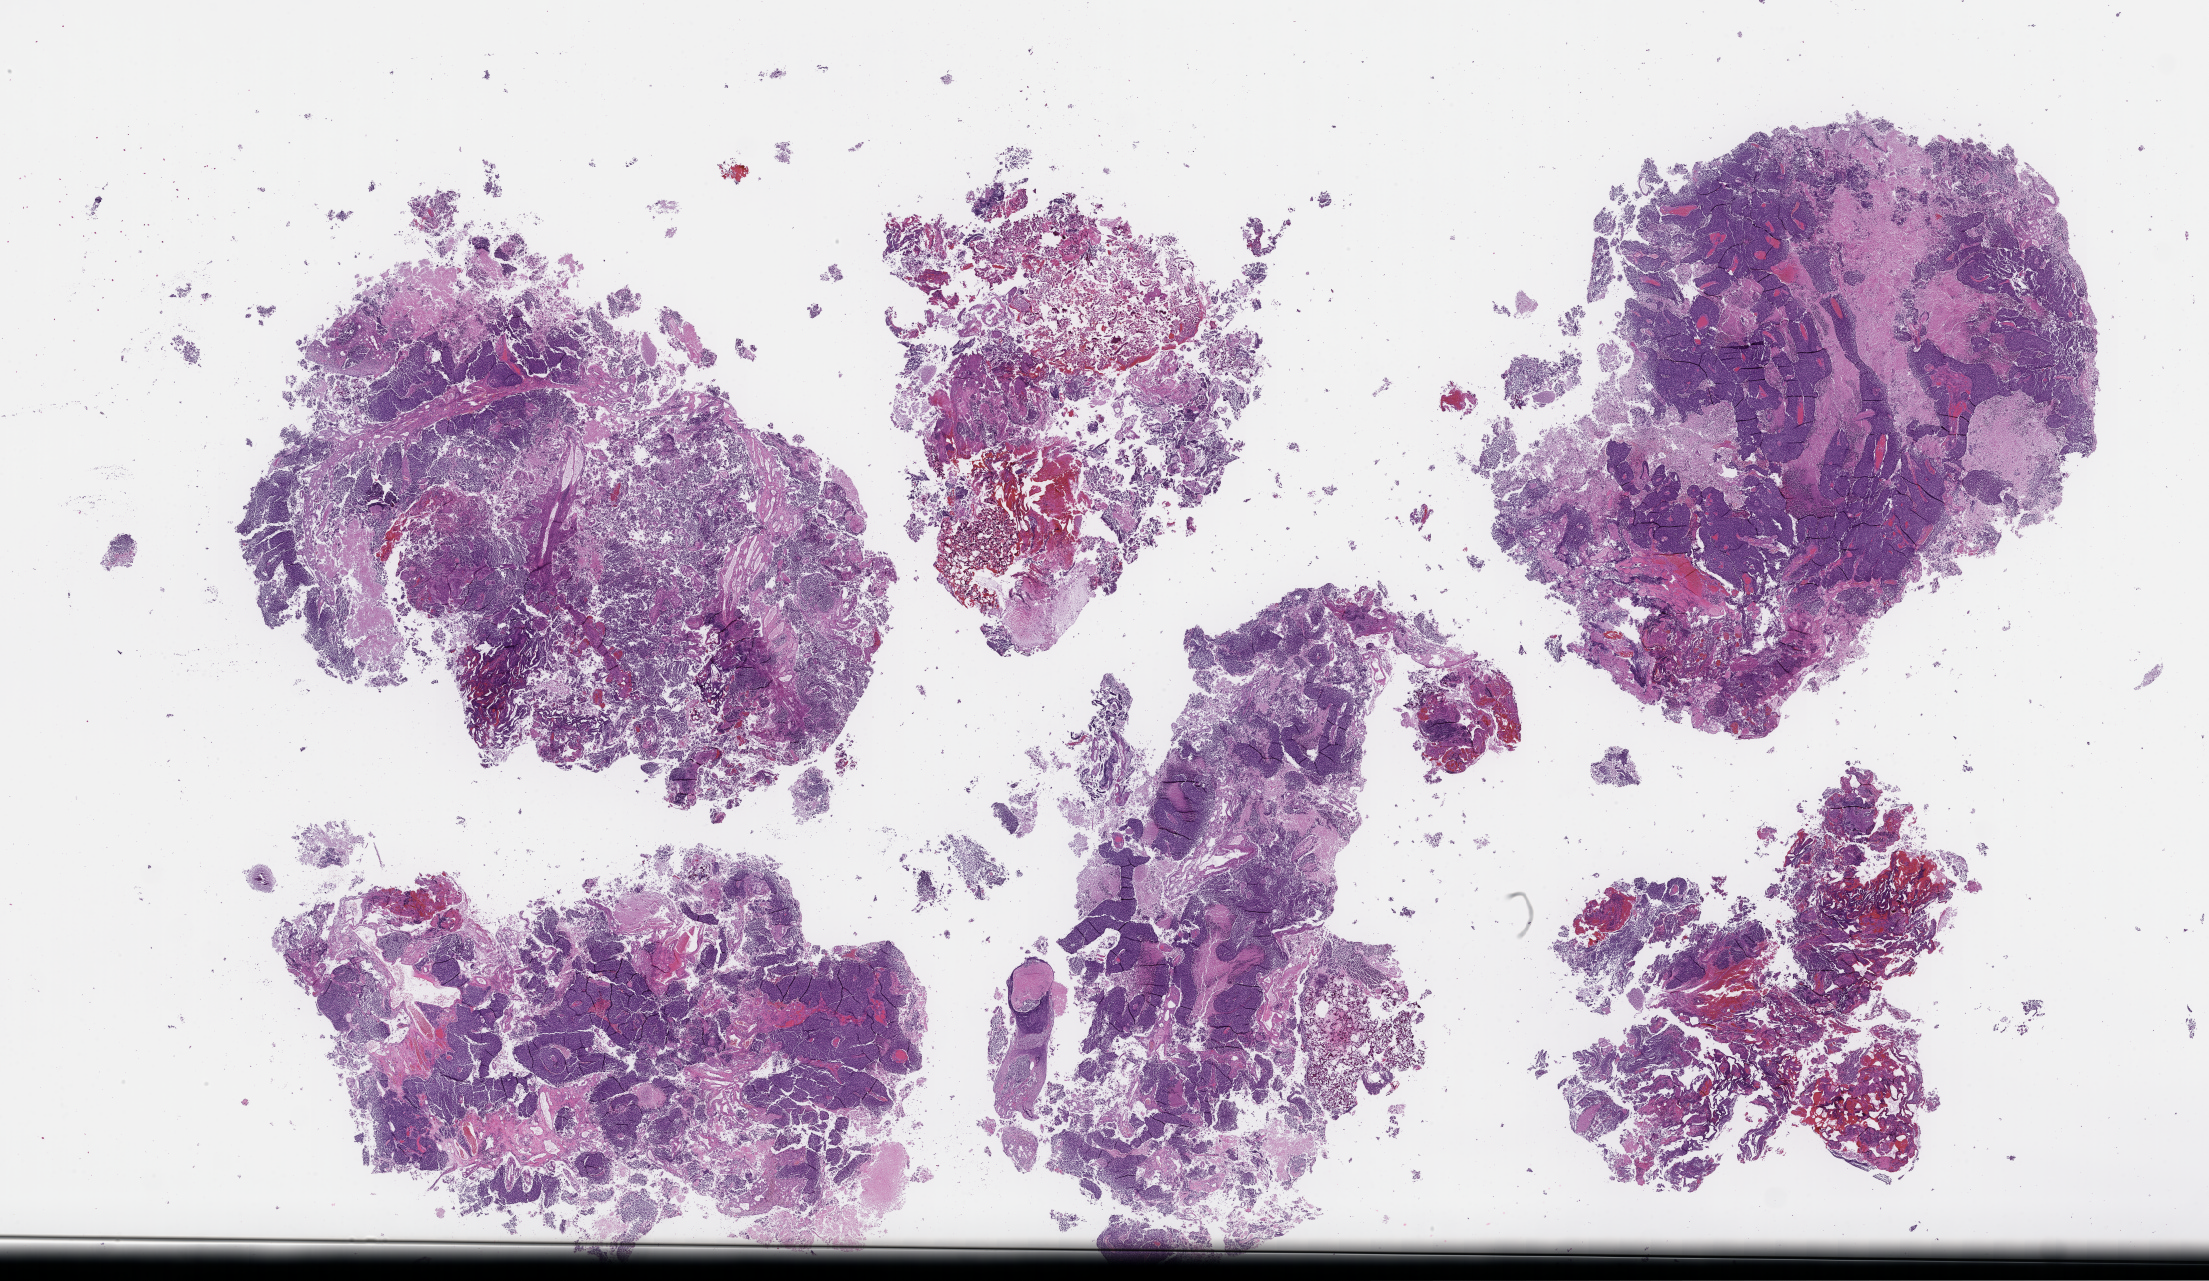
Whole-slide image, hematoxylin and eosin (H&E) stain, whole scanned area (about 35.7 x 20.7 mm) shown as a low-resolution overview. FFPE section. Archival tissue. Male patient.
This section: metastasis (sampled organ not recorded). Patient diagnosis (primary): Small Cell Lung Carcinoma.